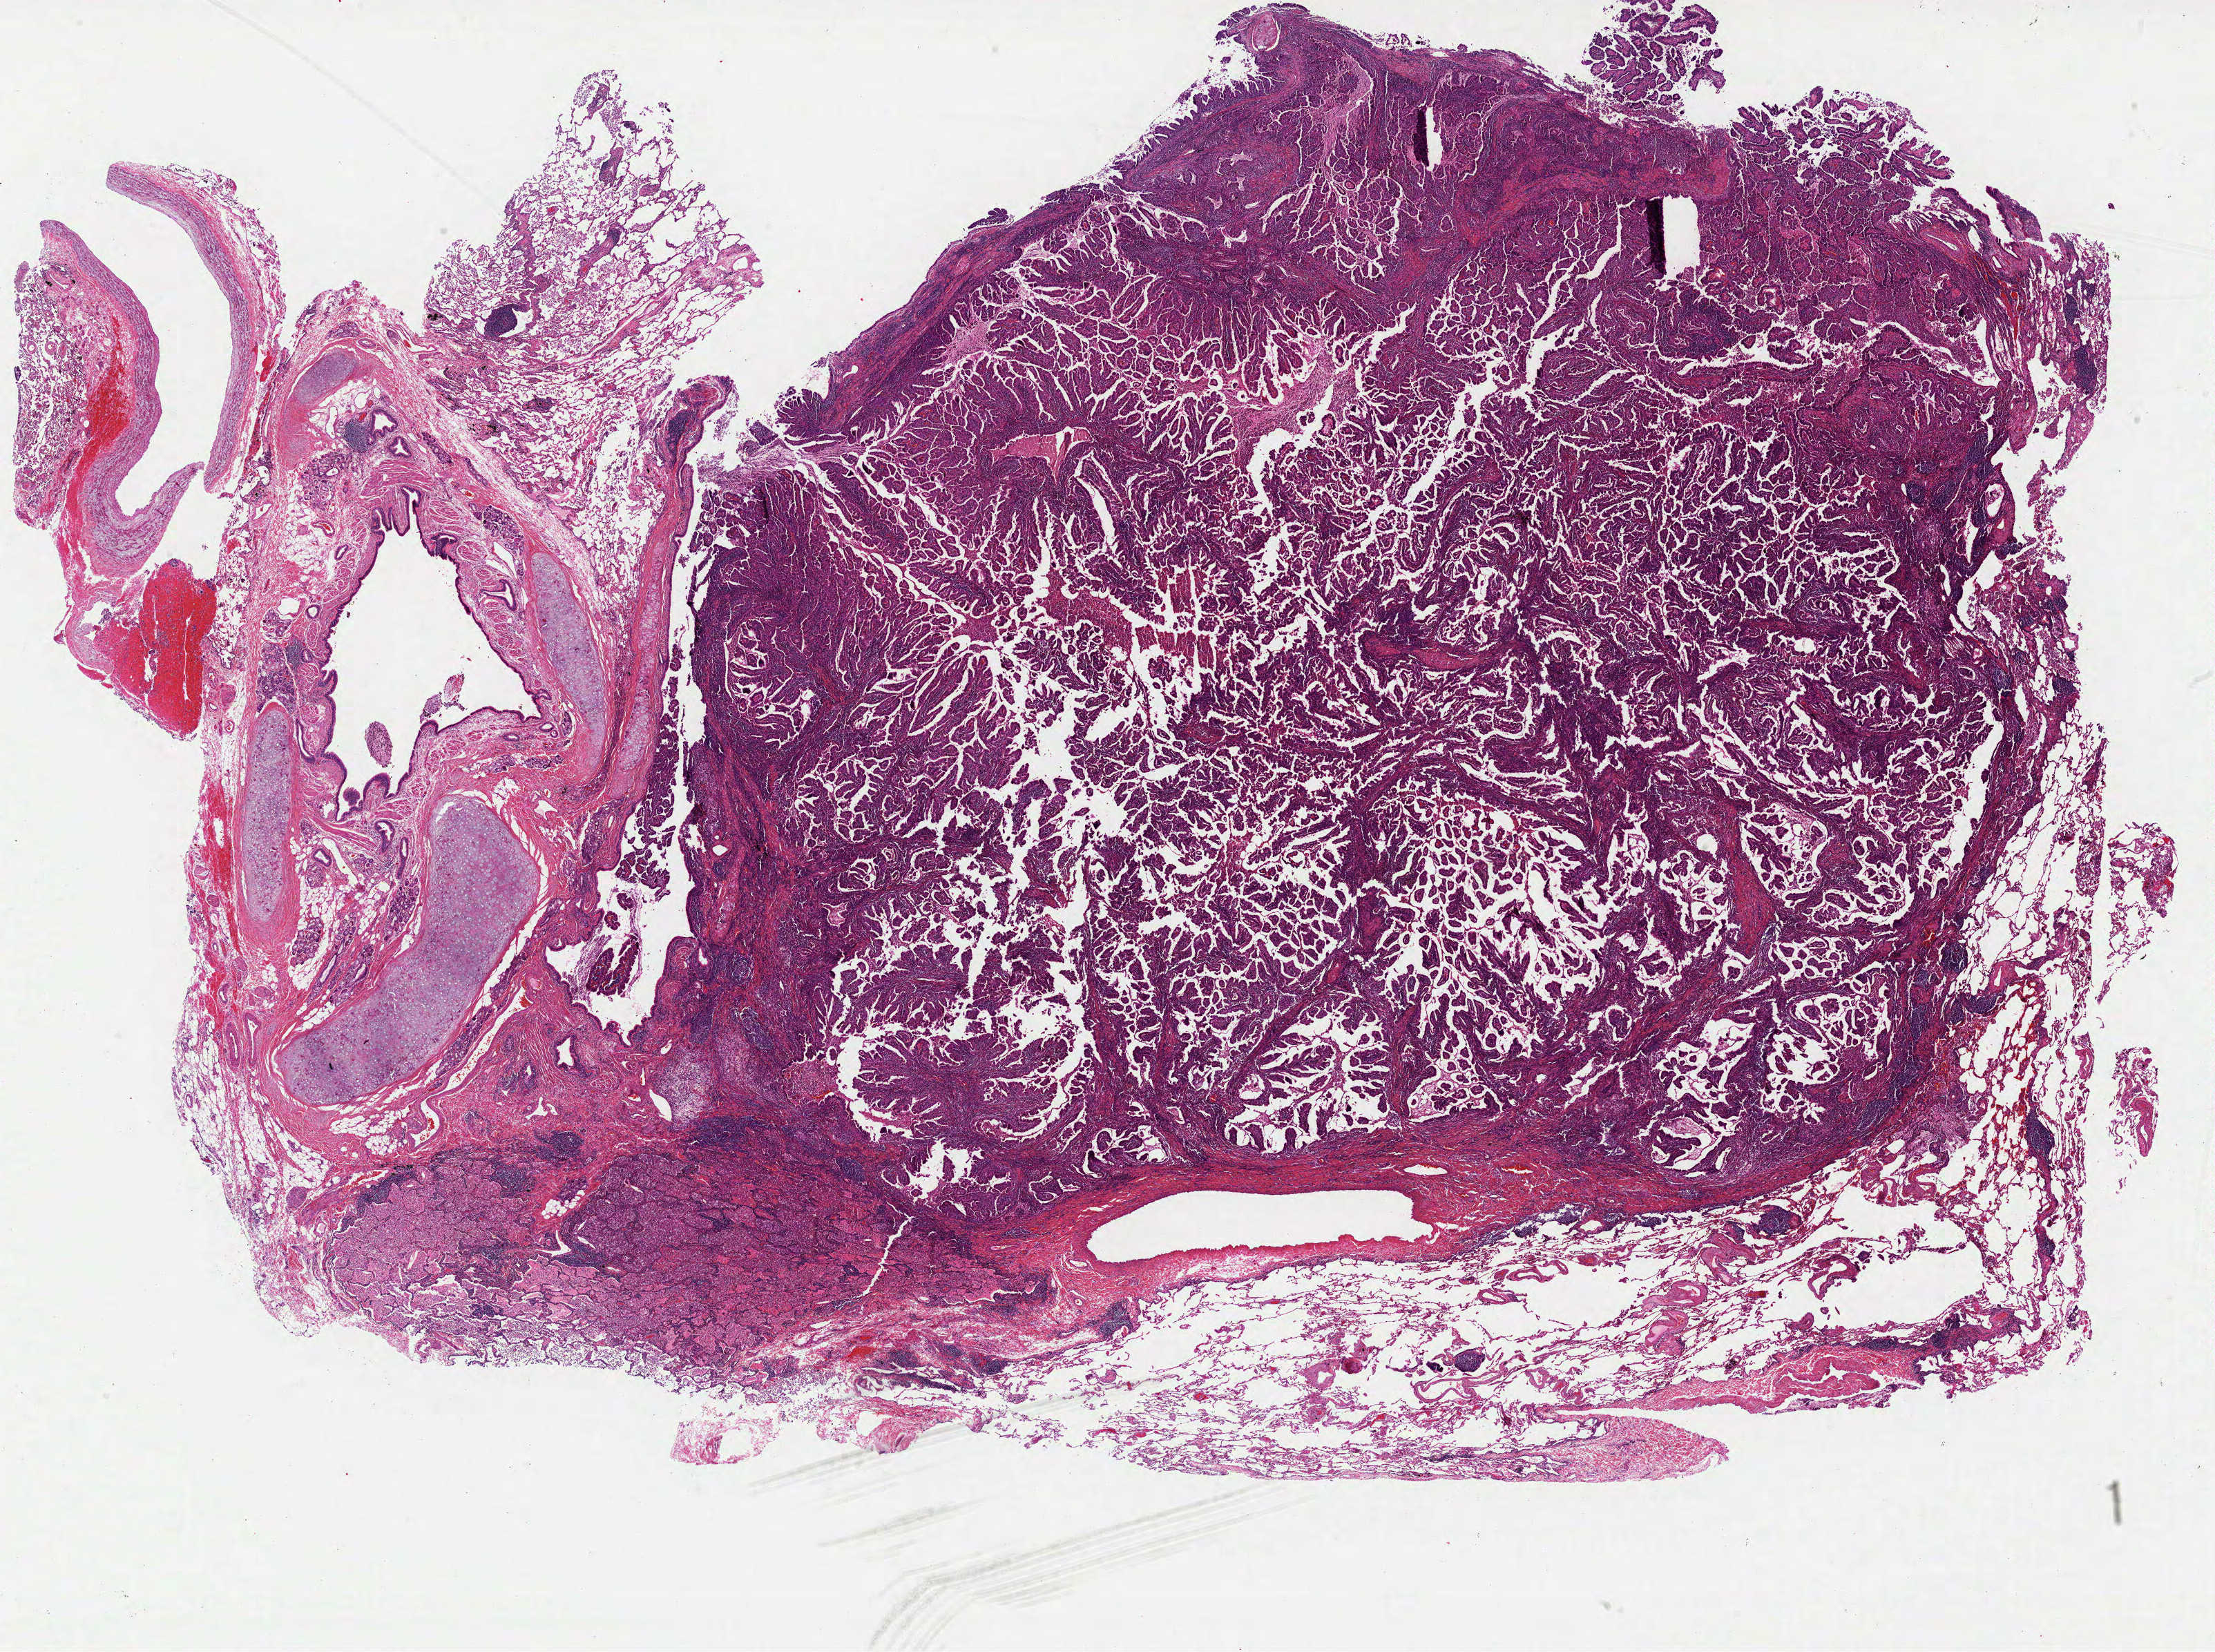
Hematoxylin and eosin (H&E) stained whole-slide image — whole scanned area (about 25.9 x 19.3 mm, acquisition: 40x scan) shown as a low-resolution overview, formalin-fixed paraffin-embedded (FFPE) diagnostic section, primary tumour sample from the lung. Female, age 79 years at initial diagnosis.
- AJCC pathologic stage: IA
- diagnosis: Papillary adenocarcinoma, NOS (upper lobe, lung)